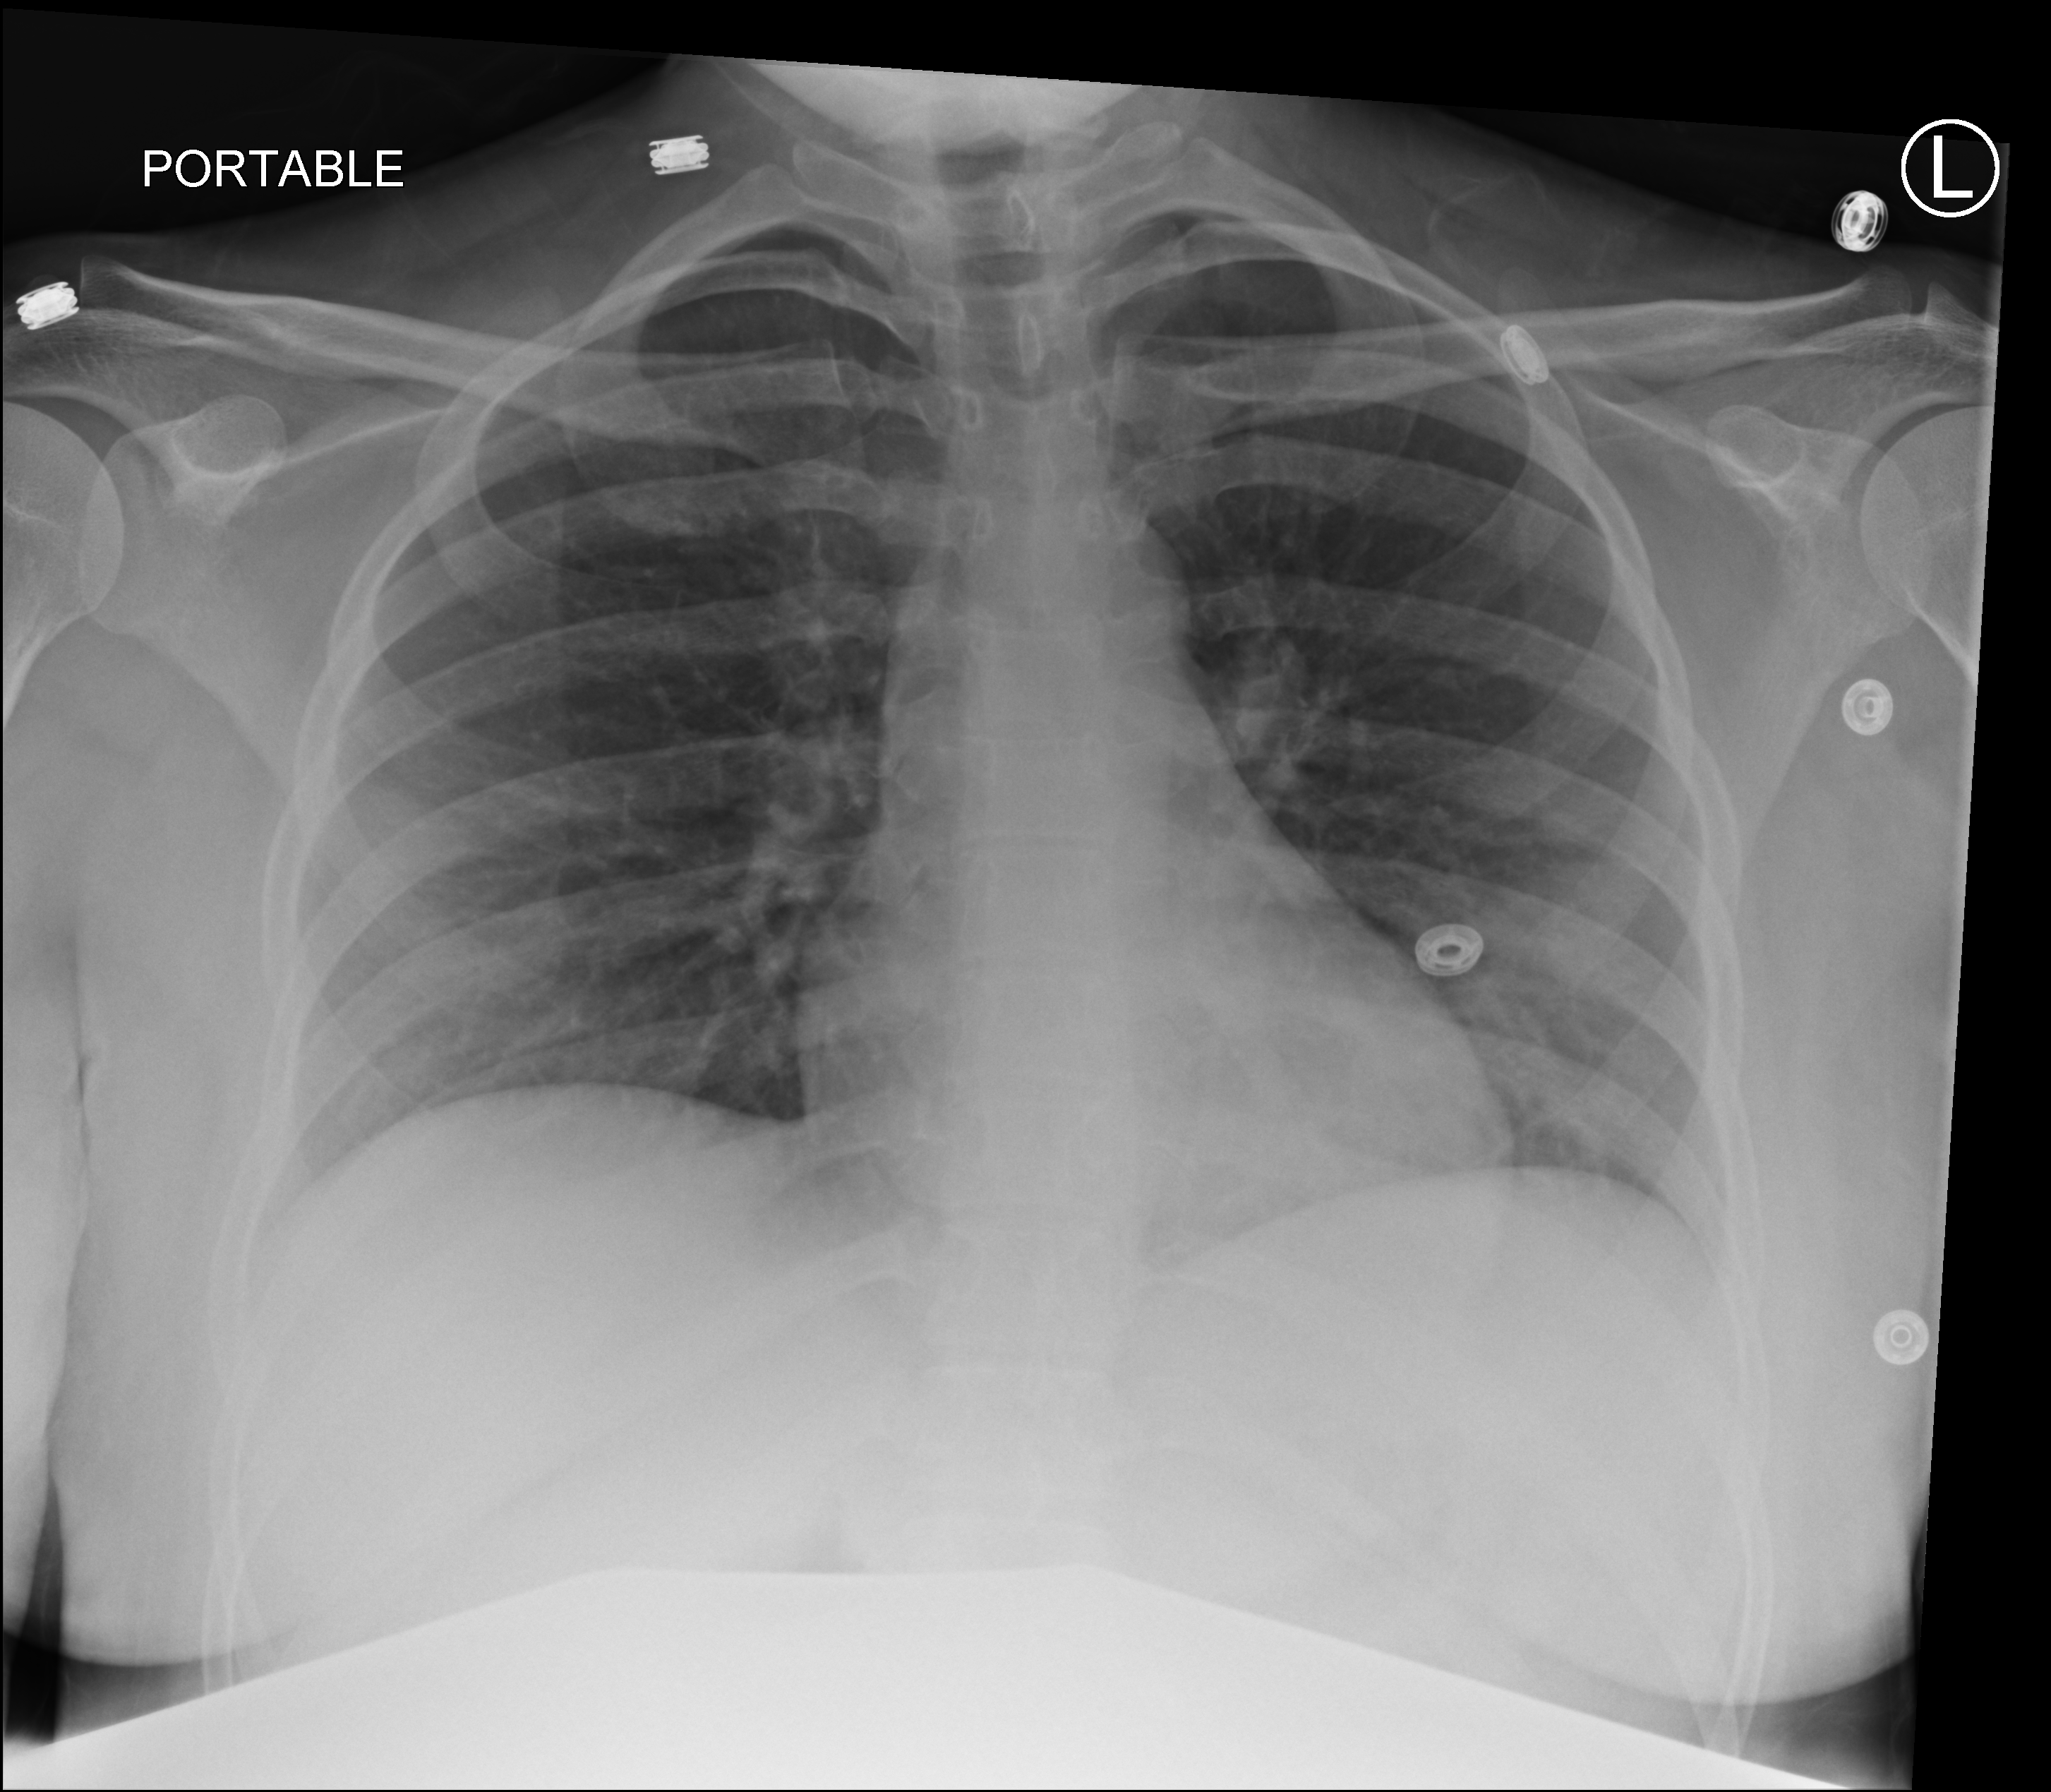
Bedside chest radiograph (computed radiography); anteroposterior (AP) projection. Female patient hospitalised with COVID-19, age 18–59 years.
Hospital-stay facts (about this admission, not read from this image; timing relative to this image not recorded): admitted to intensive care during this hospital stay: no.